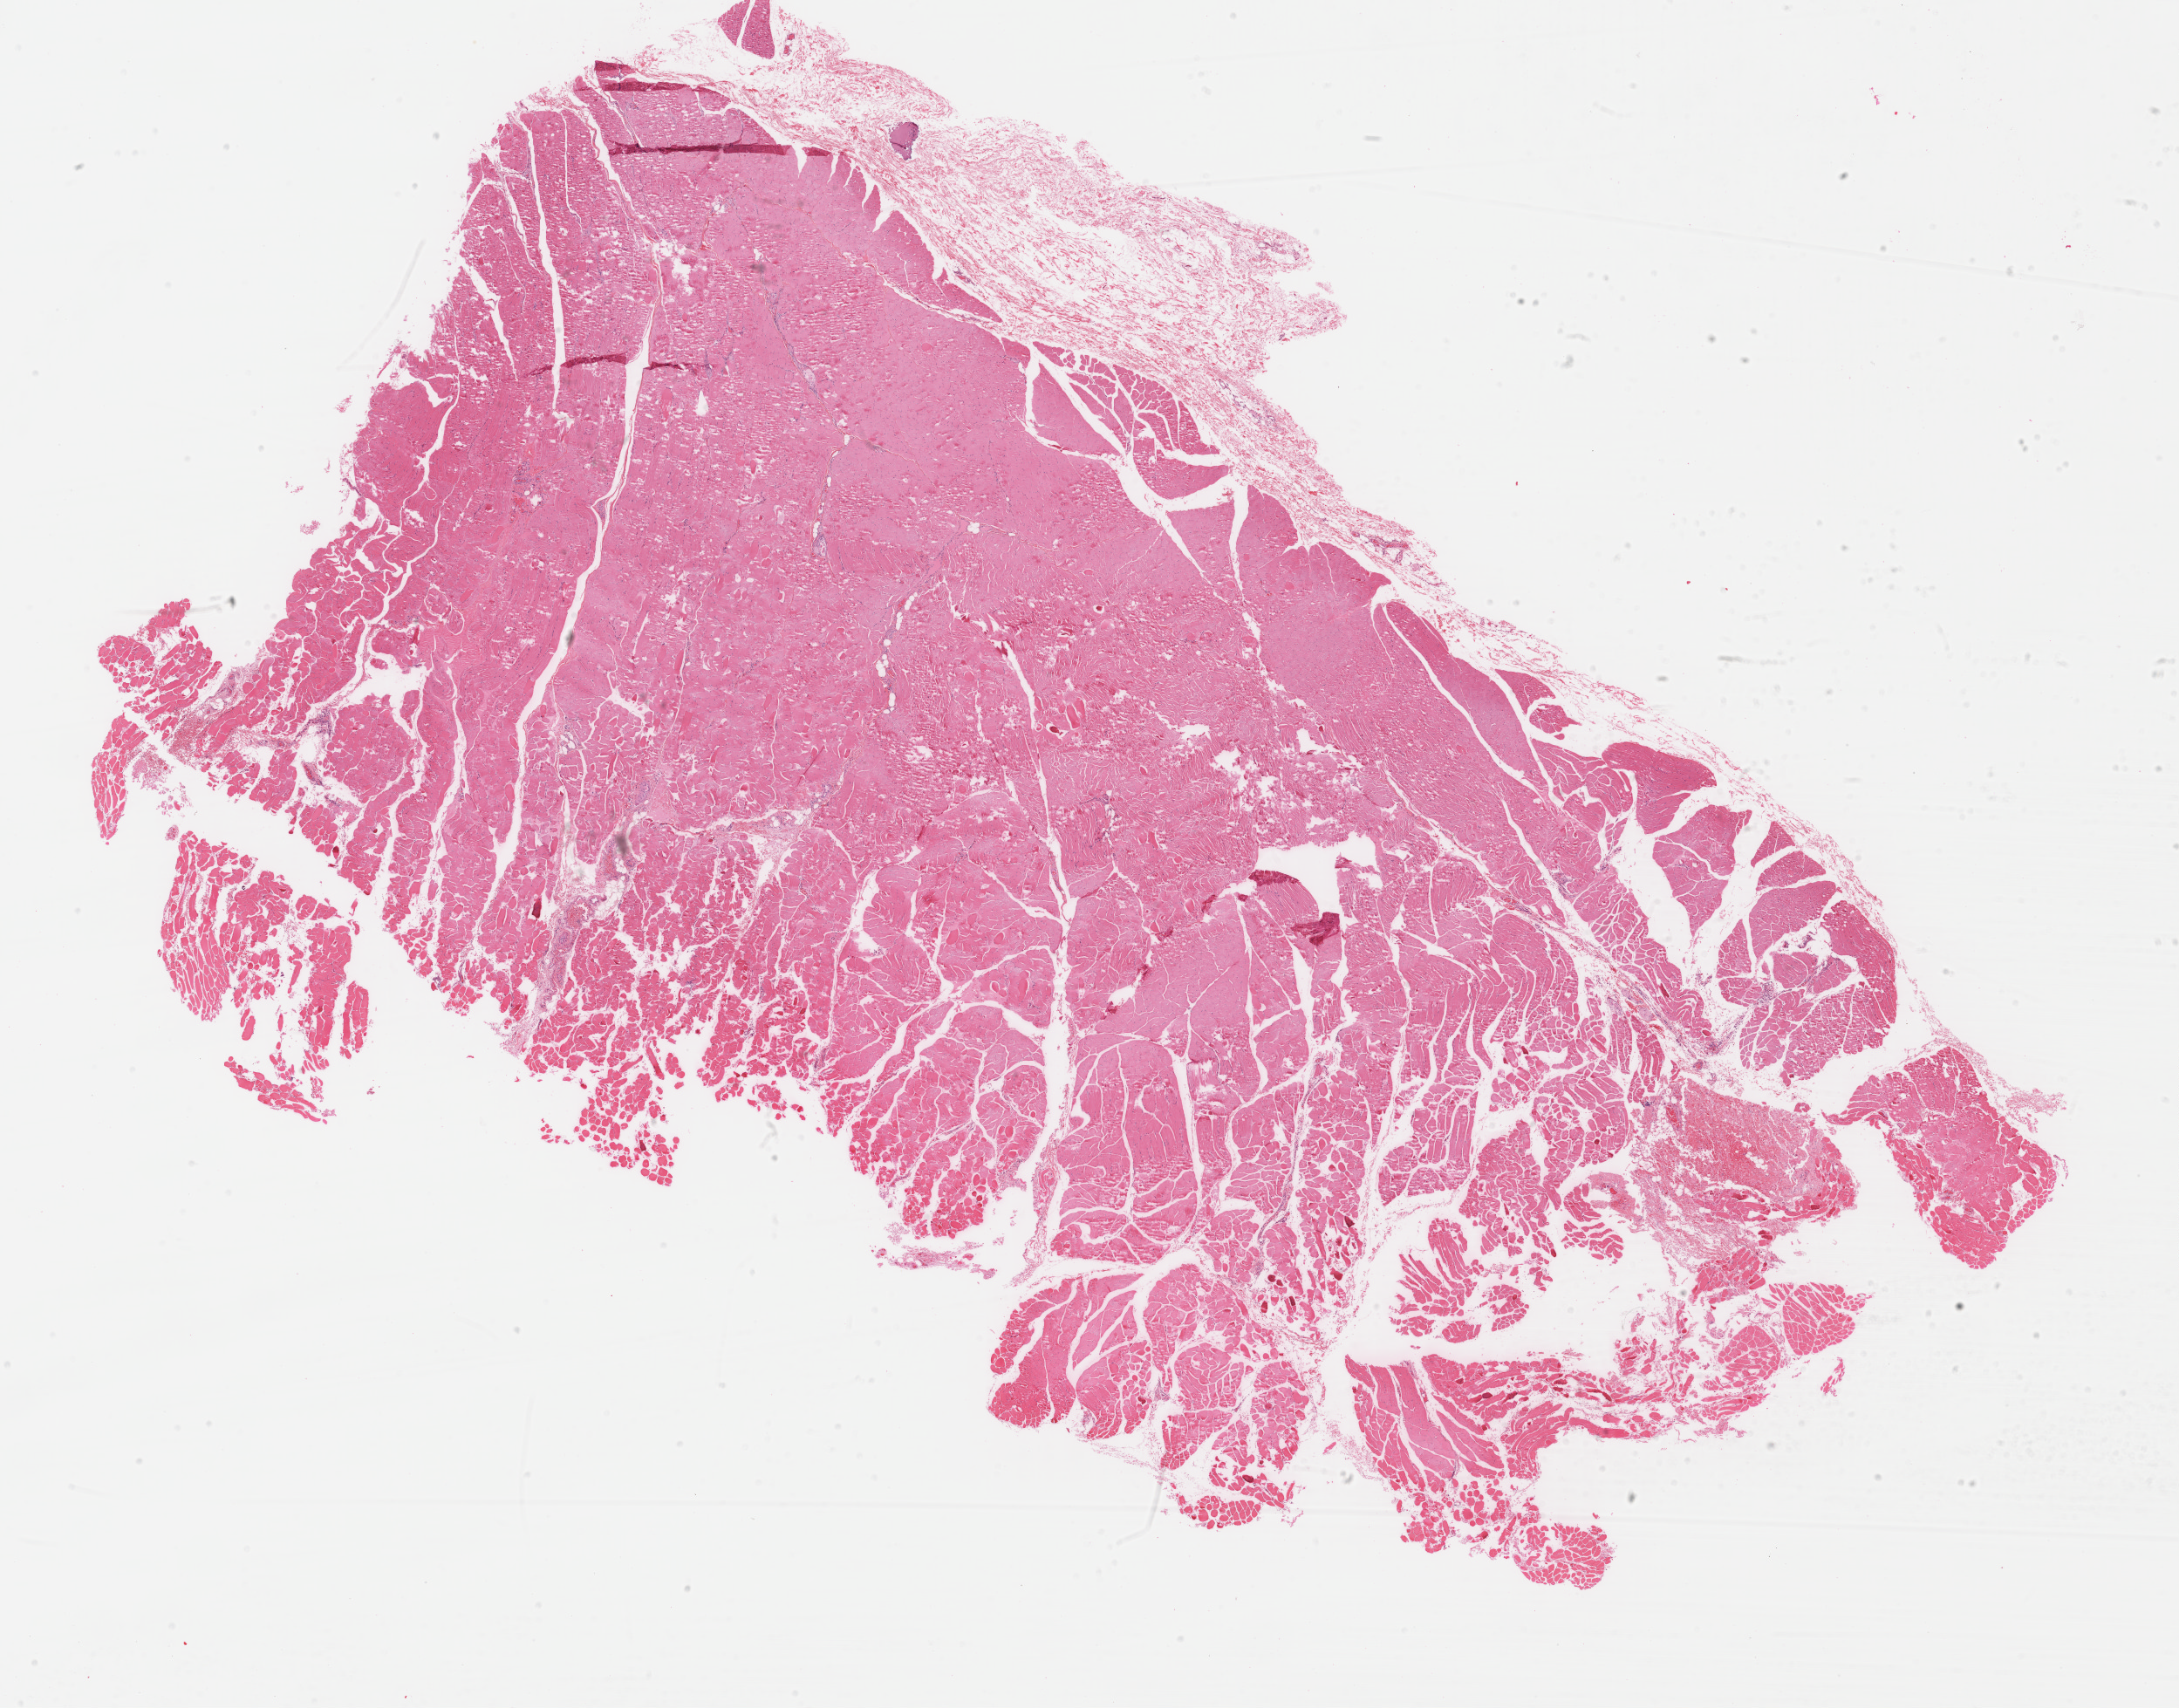
Digitized Hematoxylin and eosin (H&E) stained tissue section (whole slide) — shown as a low-resolution overview of the whole scanned area (about 19.8 x 15.5 mm). Formalin-fixed paraffin-embedded (FFPE) diagnostic section. Sample: primary tumour, thyroid. Male patient; age at initial diagnosis 28 years.
Diagnosis: Papillary adenocarcinoma, NOS (thyroid gland). AJCC pathologic stage: I. Lymph nodes positive (case pathology): 12 of 12 examined. TNM: TX N1b M0.